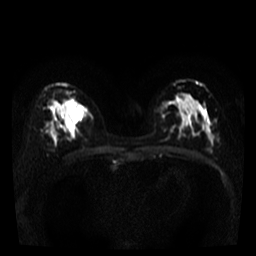
Breast MRI, one axial slice. Diffusion-weighted series; image 2 of 4 stored at this slice position (different b-values; order by instance number). 3 T. 5 mm slice thickness. 256 × 256 image matrix, field of view 280 × 280 mm. Female patient.
Outlined on this slice (manually delineated by an expert):
- tumour on diffusion-weighted imaging: box from (x=70, y=102) to (x=83, y=121) px